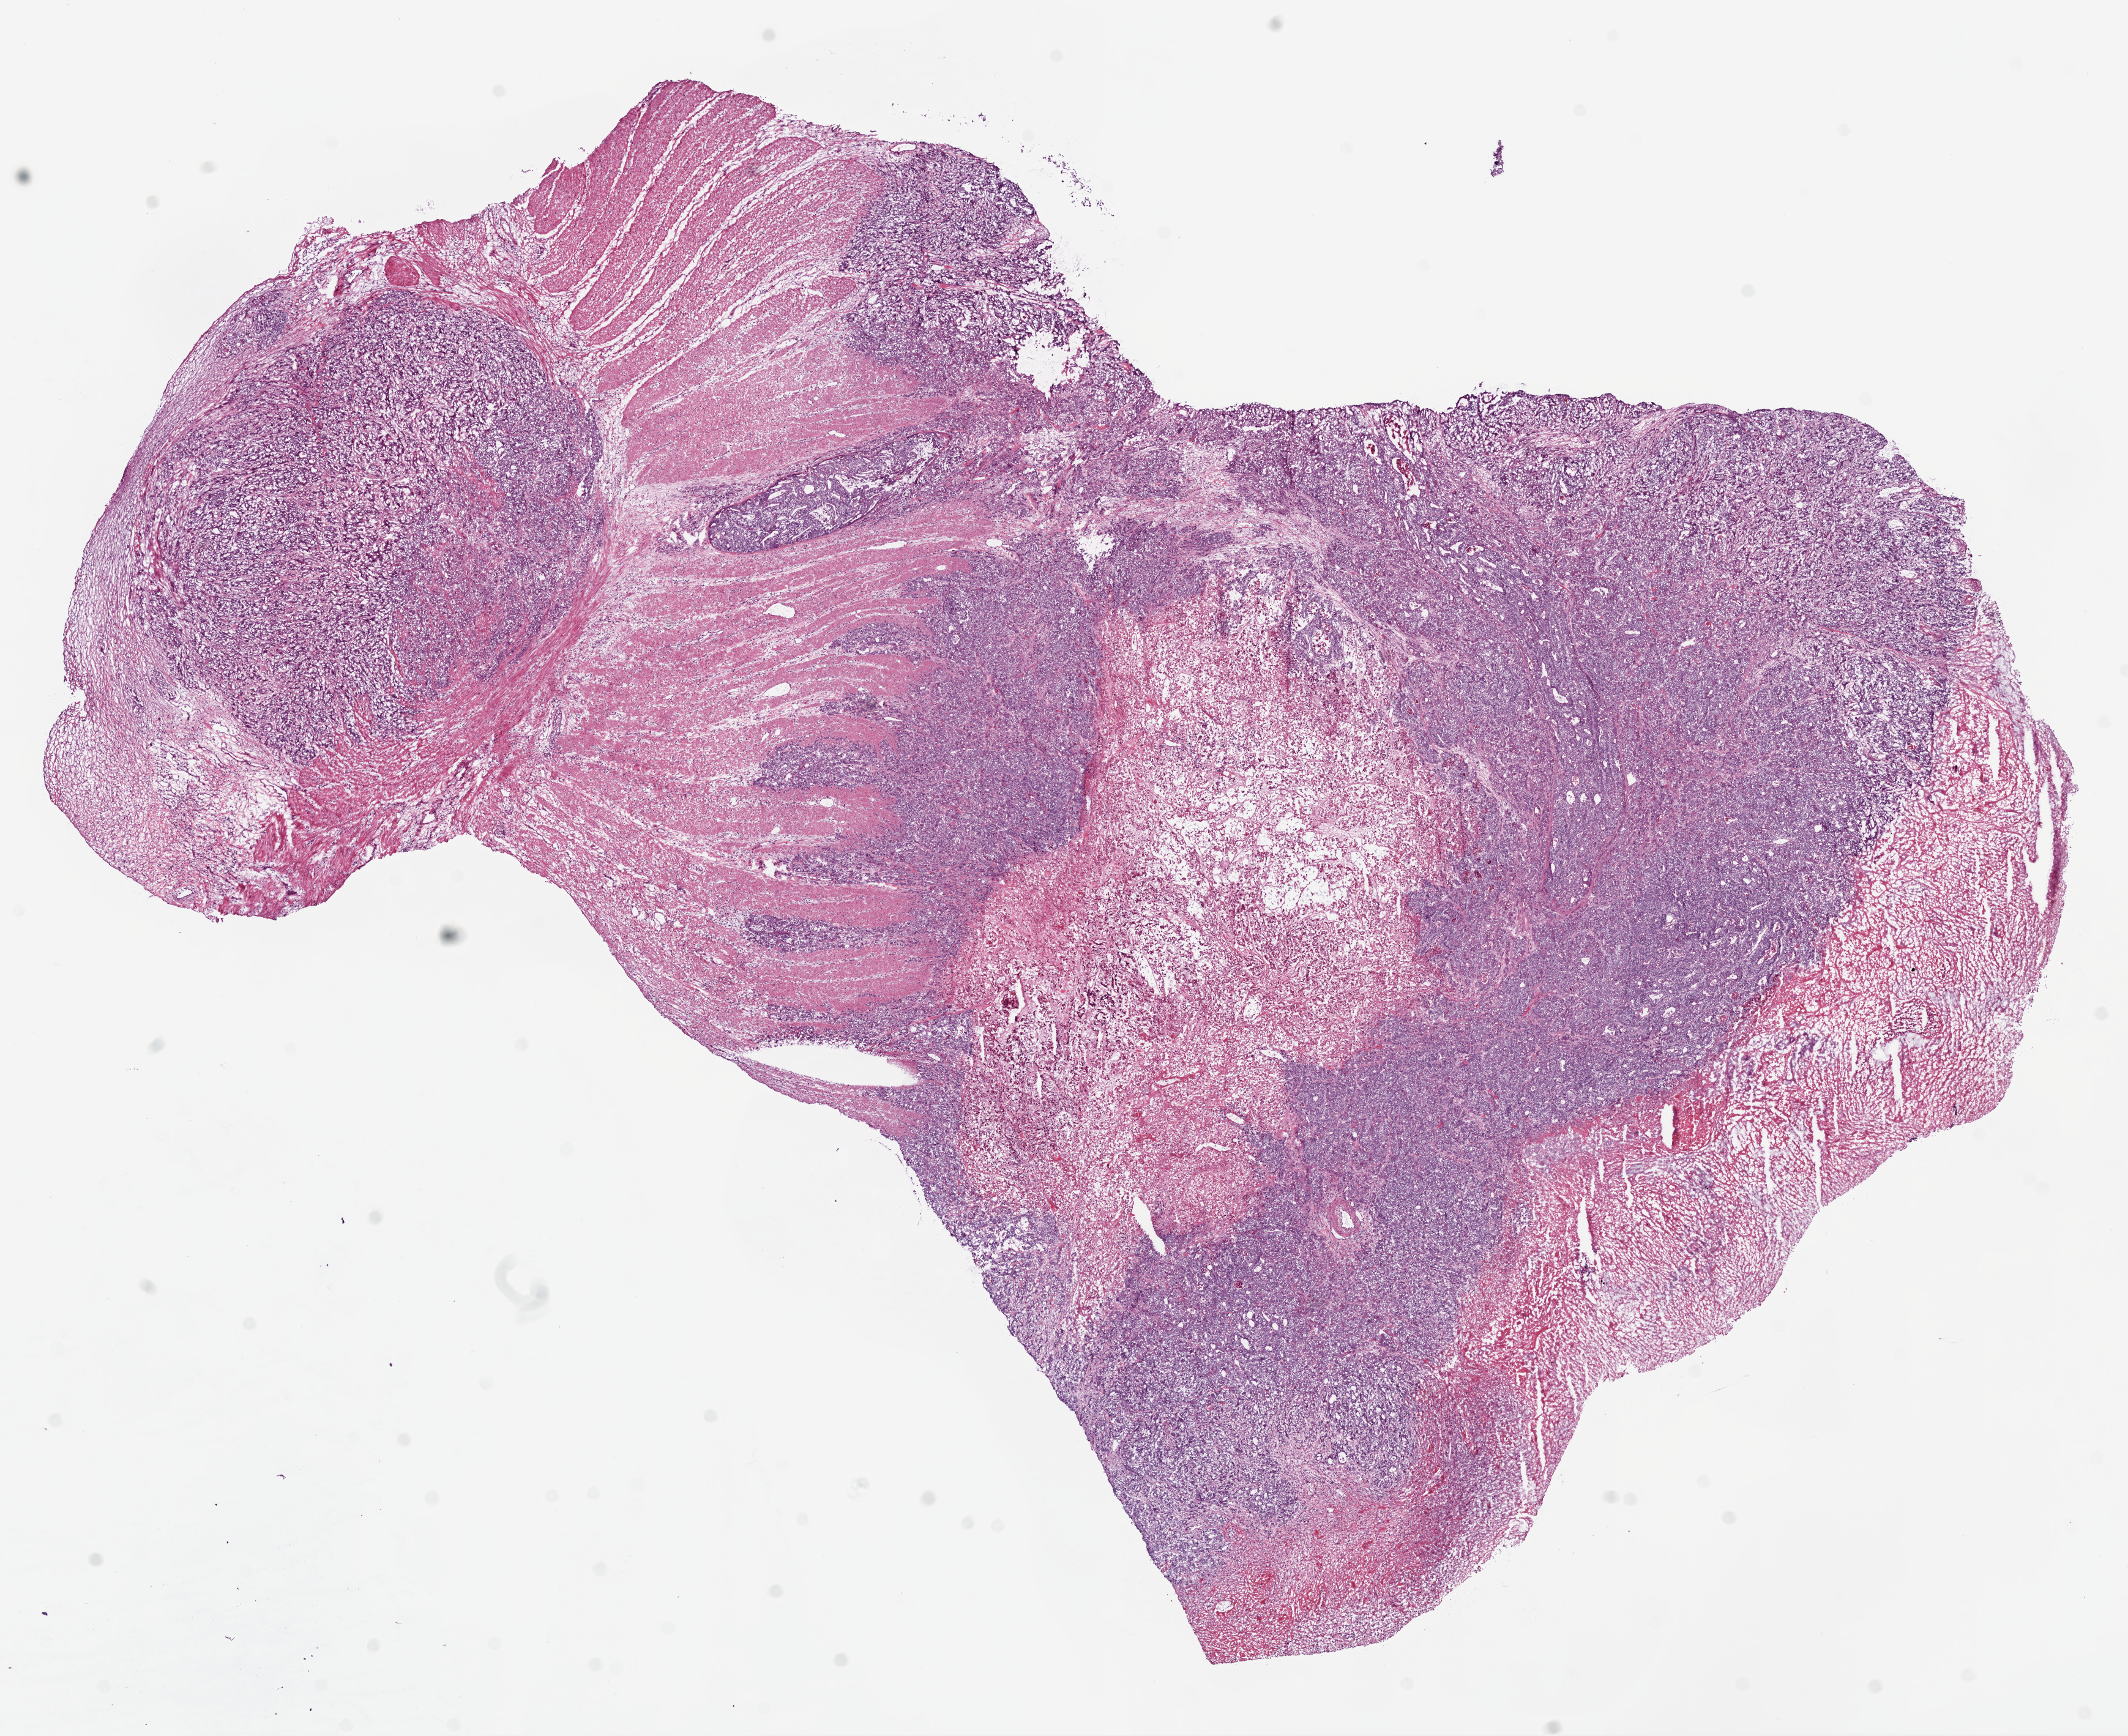
H&E-stained whole-slide image, whole scanned area (about 14.0 x 11.4 mm) shown as a low-resolution overview, frozen section, primary tumour sample from the colon. Patient: female, age at initial diagnosis 59 years. Slide review estimates, as recorded: tumour cells 60%, tumour nuclei 80%, normal cells 0%, stromal cells 15%, necrosis 25%.
- AJCC pathologic stage: IVA (7th edition)
- histologic diagnosis: Adenocarcinoma, NOS